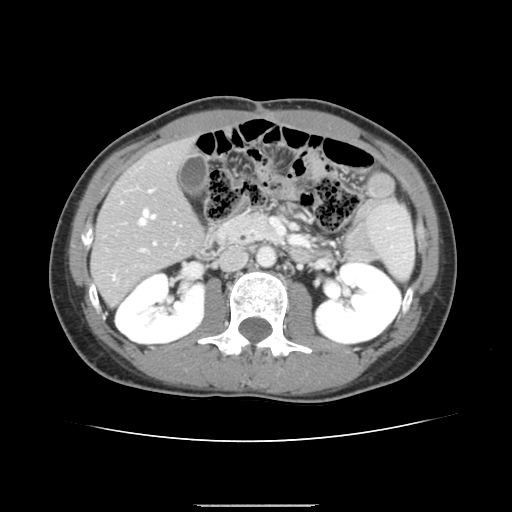
Contrast-enhanced abdominal CT, one axial slice. Slice 67 of 150 in the series (ordered by position). Intravenous contrast given. Soft-tissue window (W 400 / L 40 HU). 2.5 mm slice thickness. 512 × 512 image matrix, field of view 324 × 324 mm. Female patient, age 32 years. Case-level facts recorded for this patient, not image findings: diagnosis: colorectal cancer liver metastases, imaged before liver resection; multiple liver metastases: yes; largest metastasis: 0.7 cm.
Structures marked on this image (expert manual segmentation):
- hepatic veins: bounding box [x1, y1, x2, y2] px = [139, 209, 155, 225]
- liver: [93, 142, 201, 303]
- planned liver remnant (the part of the liver to remain after resection): [93, 141, 201, 290]
- portal vein (with intrahepatic branches): [113, 189, 156, 279]